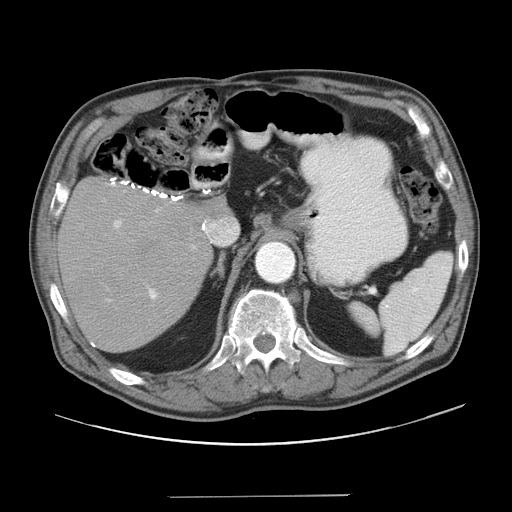
Contrast-enhanced abdominal CT, one axial slice; position 28 of 41 along the scan axis; reconstruction kernel STANDARD; 120 kVp; intravenous contrast given; soft-tissue window (W 400 / L 40 HU); 5 mm slice thickness; 512 × 512 image matrix. Male patient, age 75 years. From the clinical record (not read from this slice): diagnosis: colorectal cancer liver metastases, imaged before liver resection.
Structures marked on this image (manually delineated by an expert):
- hepatic veins: bounding box <204,217,236,246> (left, top, right, bottom; pixels)
- liver: <61,183,210,351>
- planned liver remnant (the part of the liver to remain after resection): <61,183,210,351>
- portal vein (with intrahepatic branches): <106,208,162,302>